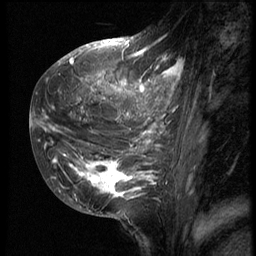
Breast MRI (dynamic contrast-enhanced), one sagittal slice. Position 20 of 62 along the scan axis. 3 images stored at this slice position (order not interpretable as contrast timing). 1.5 T. TE 4.2 ms, TR 9 ms. 256 × 256 image matrix. Female patient, age 28 years. From the clinical record (not read from this slice): setting: breast cancer imaged before/during neoadjuvant chemotherapy.
Annotated regions visible in this slice (semi-automatically segmented with operator editing):
- analysis volume of interest (the breast-tissue region the enhancement analysis was run in; not a lesion): bounding box (x1, y1, x2, y2) in pixels: (42, 48, 187, 207)
- tumour enhancement mask (voxels above the 140 % enhancement threshold inside the analysis volume of interest): (42, 48, 183, 199)